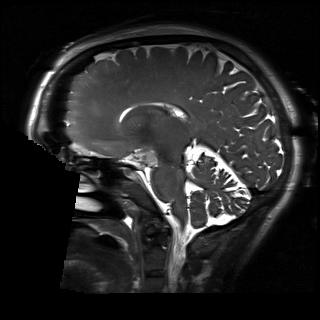
Brain MRI from a brain-tumour surgery series, one sagittal slice; position 105 of 192 along the scan axis; 320 × 320 image matrix, field of view 230 × 230 mm. Case-level facts recorded for this patient, not image findings: histopathology: Glioblastoma; WHO grade: 2; IDH mutation: no.
Annotated regions visible in this slice (expert manual segmentation):
- residual tumour: bounding box <138,152,157,163> (left, top, right, bottom; pixels)